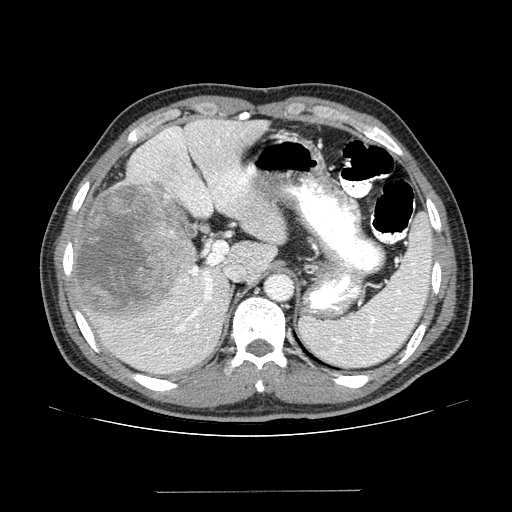
Contrast-enhanced abdominal CT (liver protocol), one axial slice; position 95 of 131 along the scan axis; reconstruction kernel STANDARD; one of 2 acquisitions stored at this slice position; soft-tissue window (W 400 / L 40 HU); 2.5 mm slice thickness; 512 × 512 image matrix. From the clinical record (not read from this slice): diagnosis: hepatocellular carcinoma (patient treated with transarterial chemoembolisation; whether this scan precedes or follows treatment is not stated here); TNM stage (as recorded): Stage-I; Child-Pugh class: A; tumour differentiation: poorly differentiated.
Structures marked on this image (semi-automatic segmentation, software-assisted and operator-edited):
- liver parenchyma outside the tumour (the mass and vessels are separate outlines, so this box may not span the whole liver): bounding box <68,118,284,374> (left, top, right, bottom; pixels)
- mass: <72,184,195,320>
- liver vessels: <68,127,249,354>